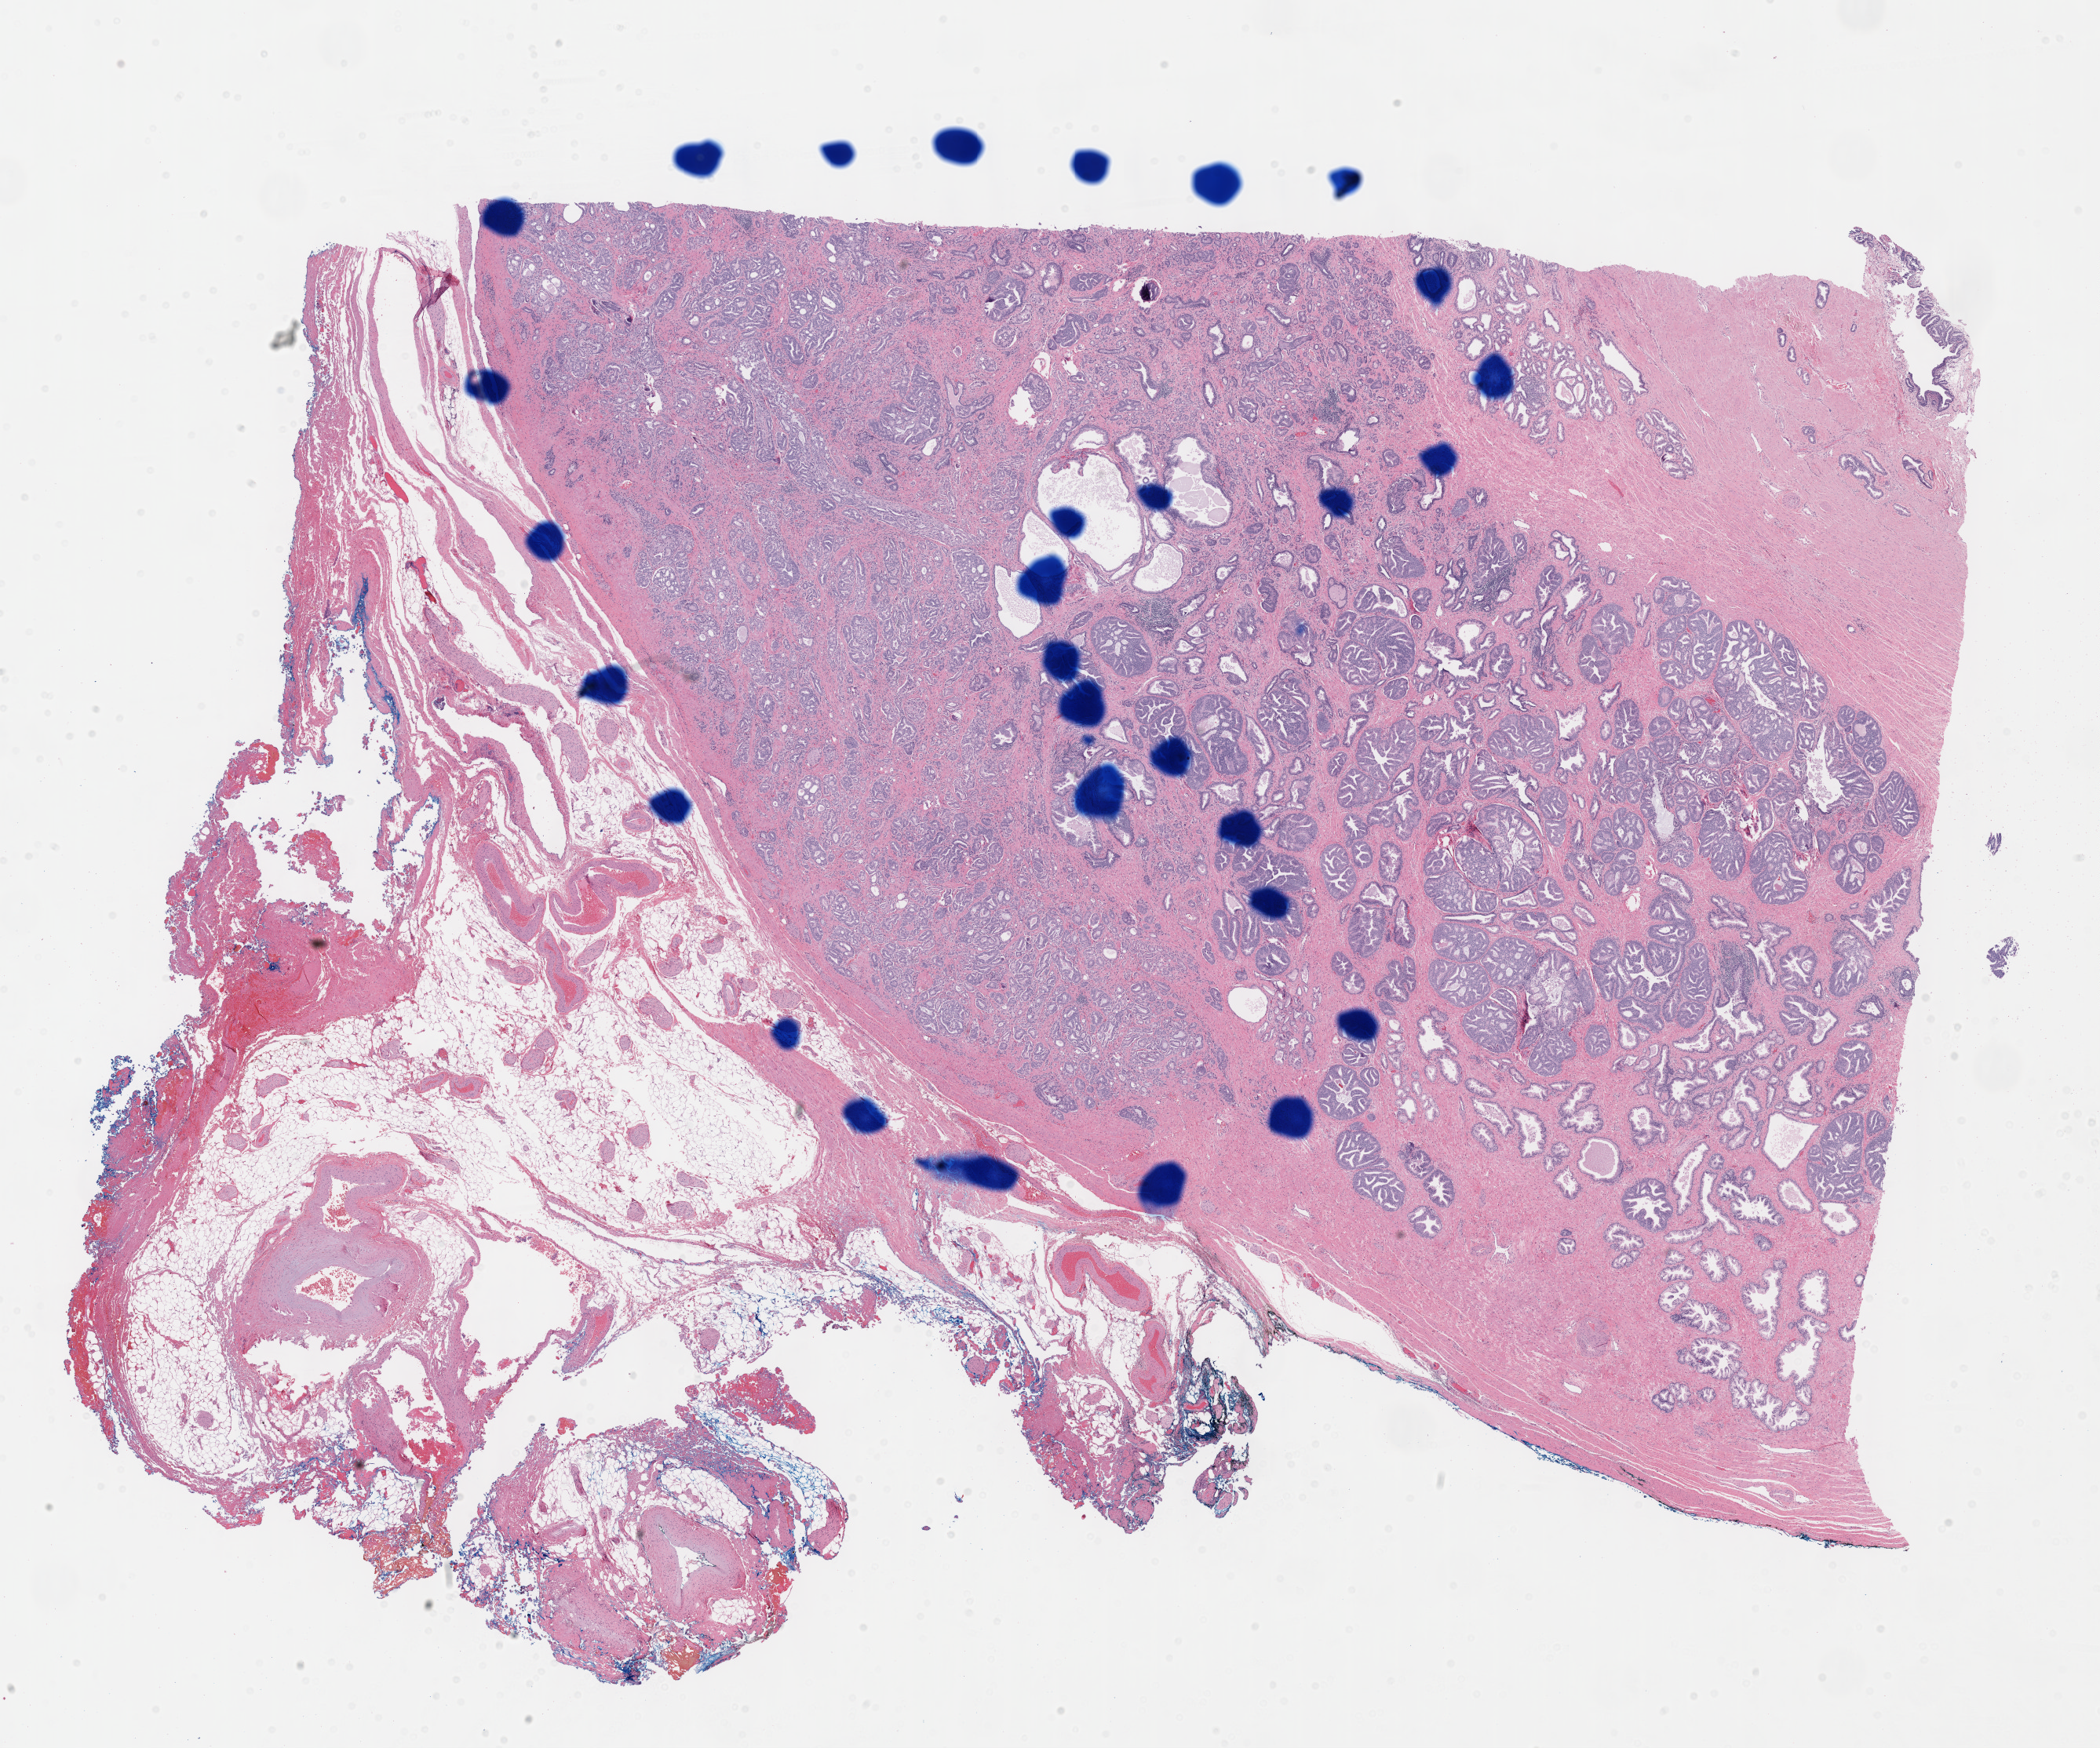
Digitized H&E-stained tissue section (whole slide) — shown as a low-resolution overview of the whole scanned area (about 21.6 x 18.0 mm), formalin-fixed paraffin-embedded (FFPE) diagnostic section, prostate, primary tumour sample. Male, age 59 years at initial diagnosis.
Histologic diagnosis: Adenocarcinoma, NOS (prostate gland).